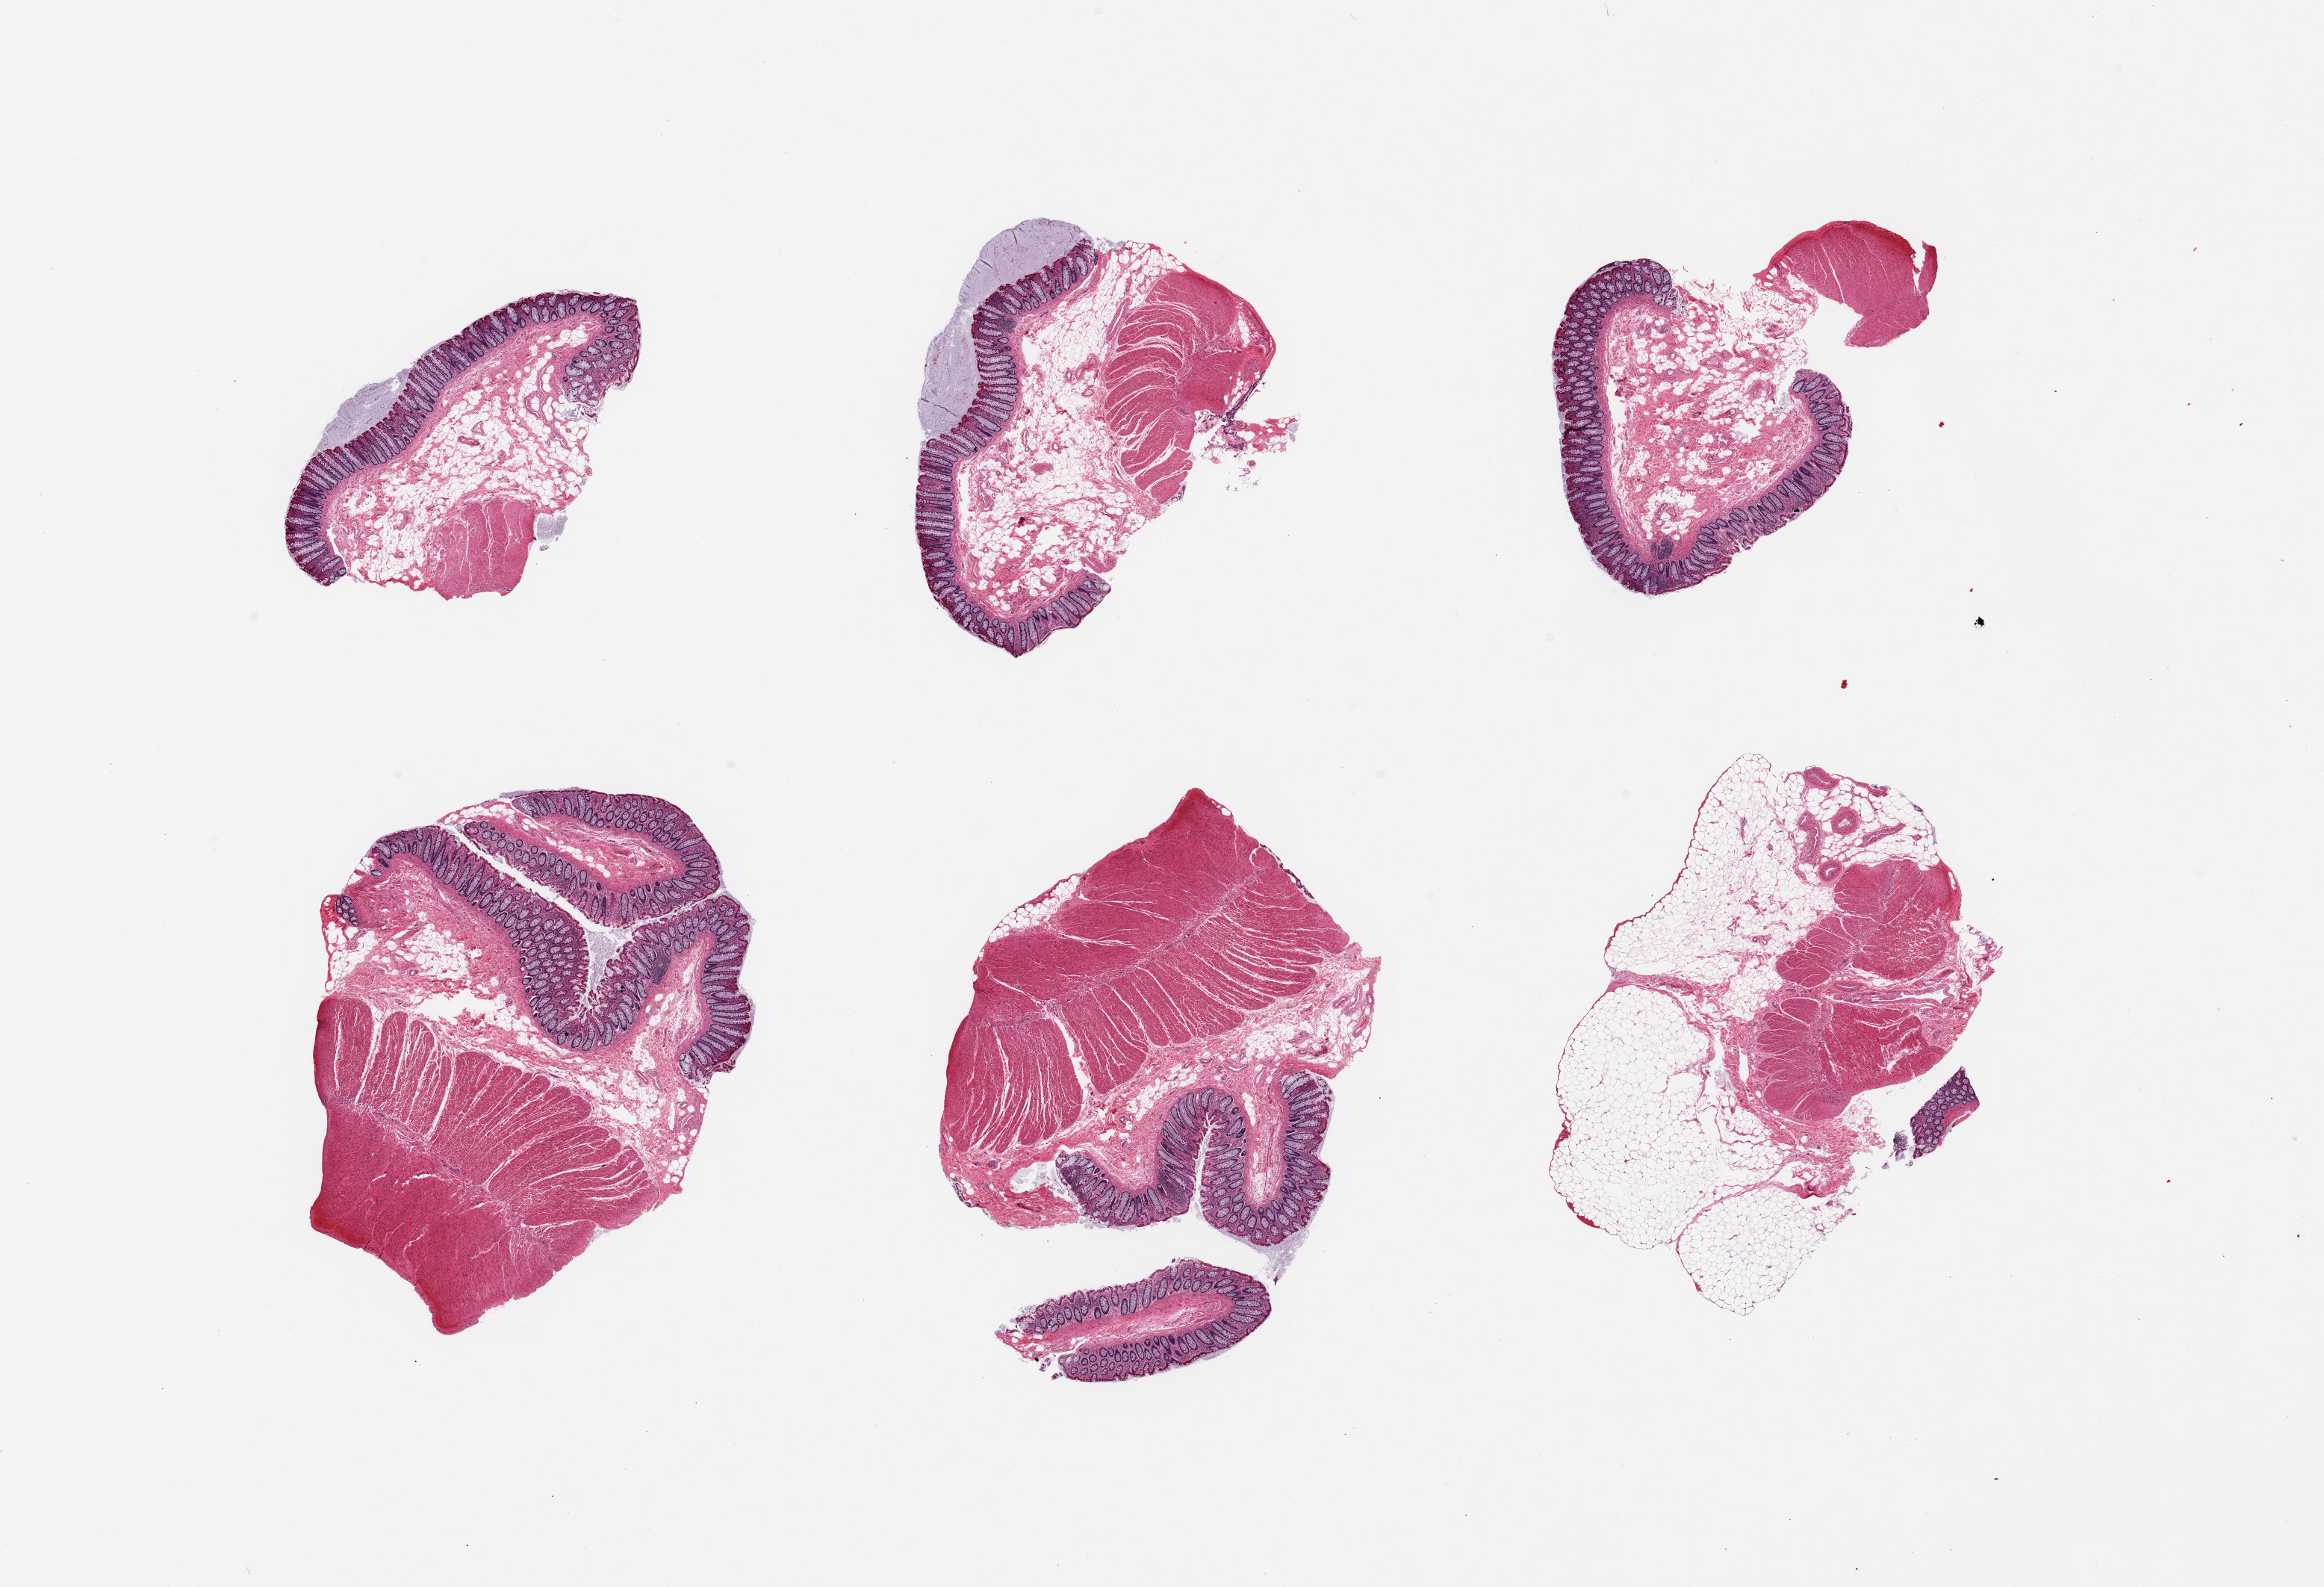
Whole-slide image, hematoxylin and eosin (H&E) stain, brightfield — a low-resolution overview of the entire scanned area, about 24.6 x 16.8 mm (from a 20x scan), PAXgene-fixed paraffin-embedded (PFPE) section, section of ileum (target tissue), donor tissue sample.
* pathologist's review note for this sample: 6 pieces, not ileum, sections of colon and muscularis